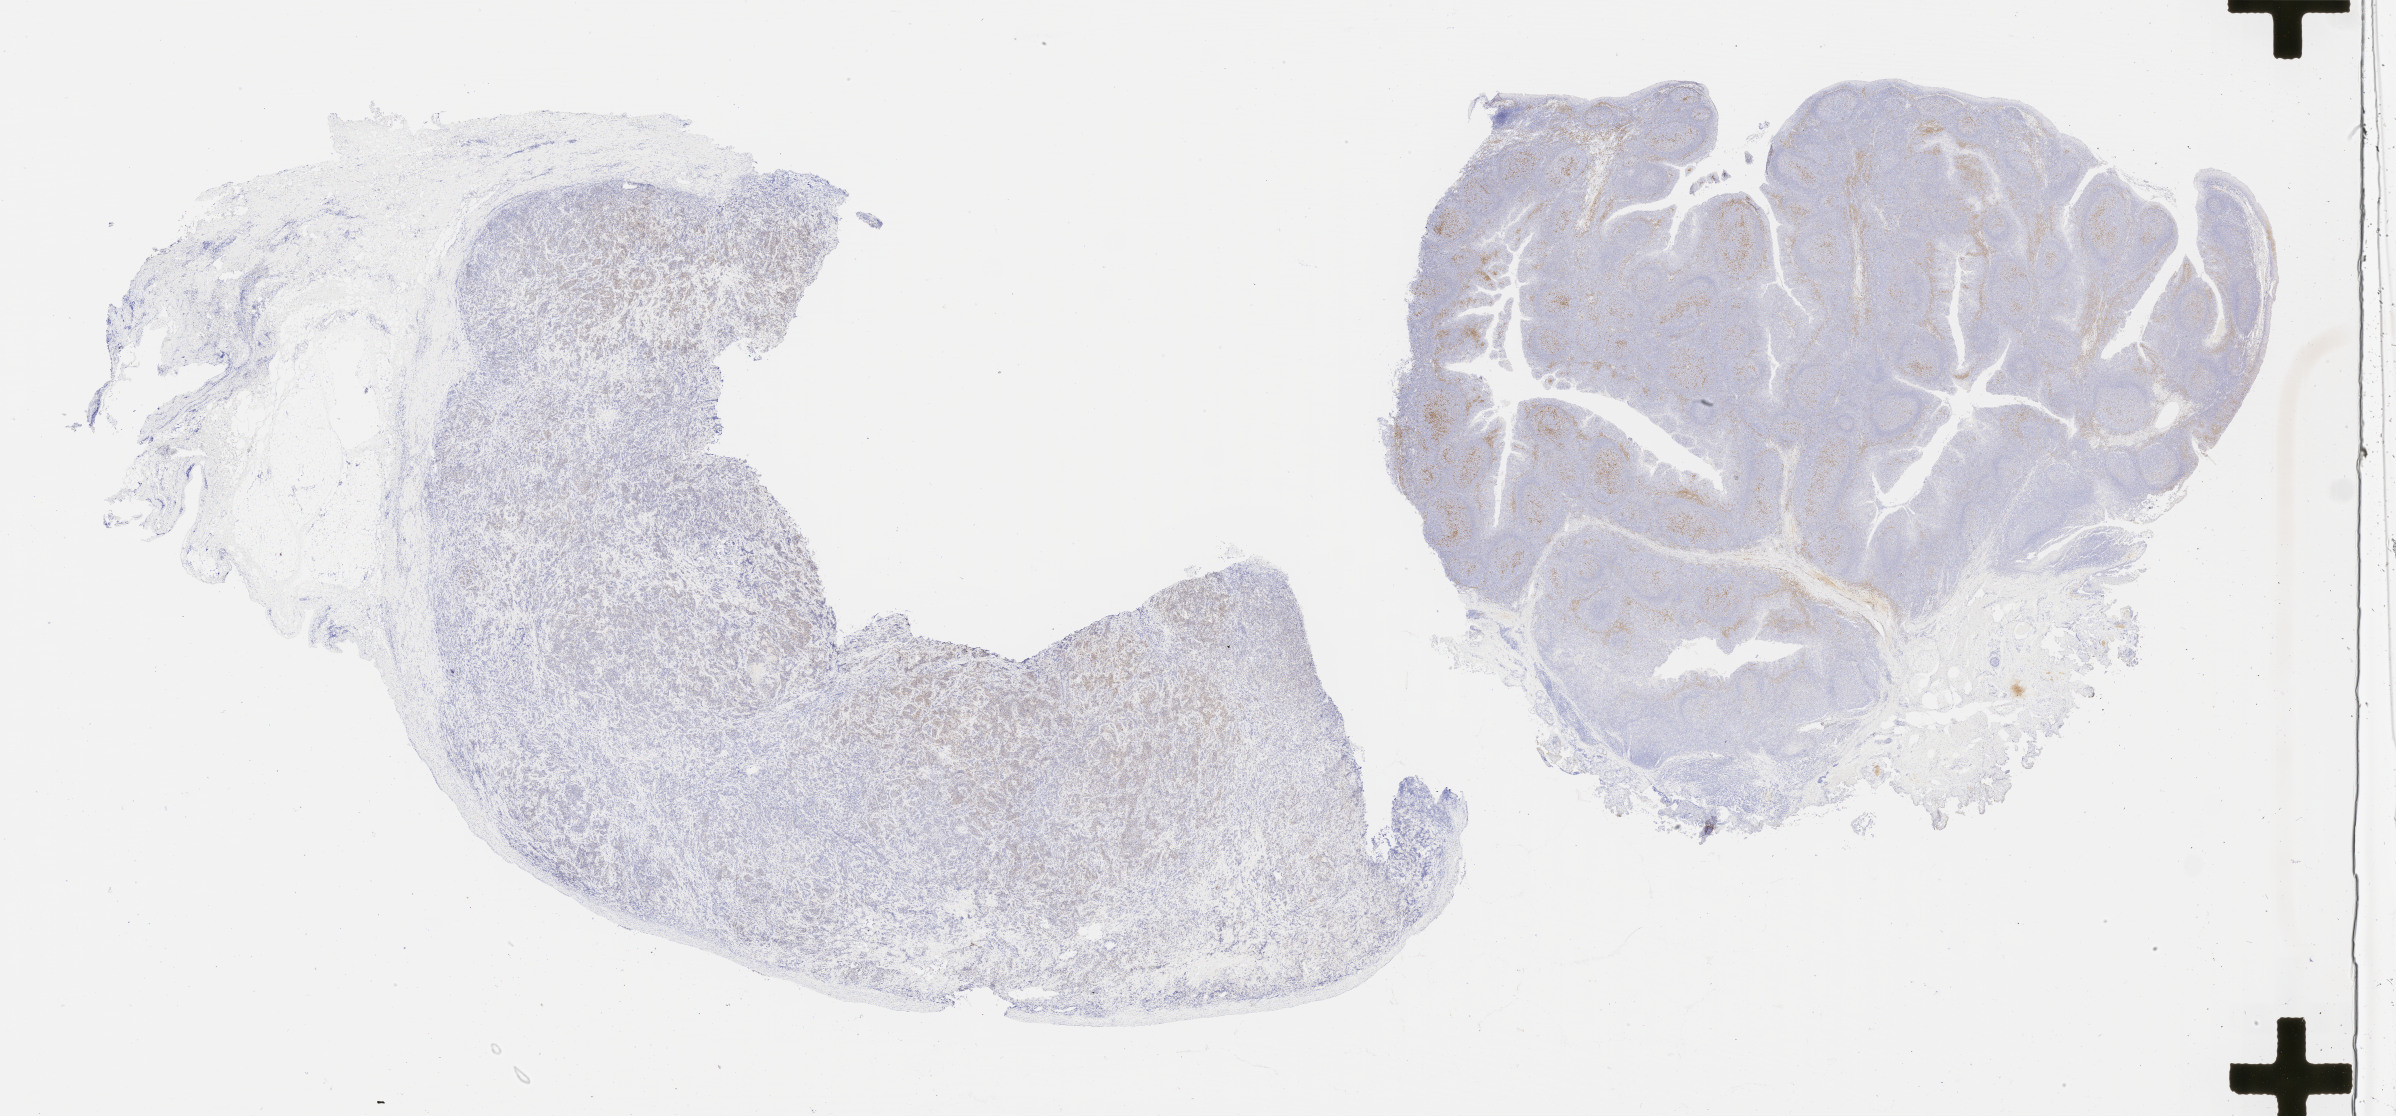
IHC for IRF4/MUM1, whole-slide image, shown as a low-resolution overview of the whole scanned area (about 38.7 x 18.0 mm), specimen: tumor tissue, site: bone. Patient male; aged 48.
• diagnosis: Diffuse large B-cell lymphoma, NOS